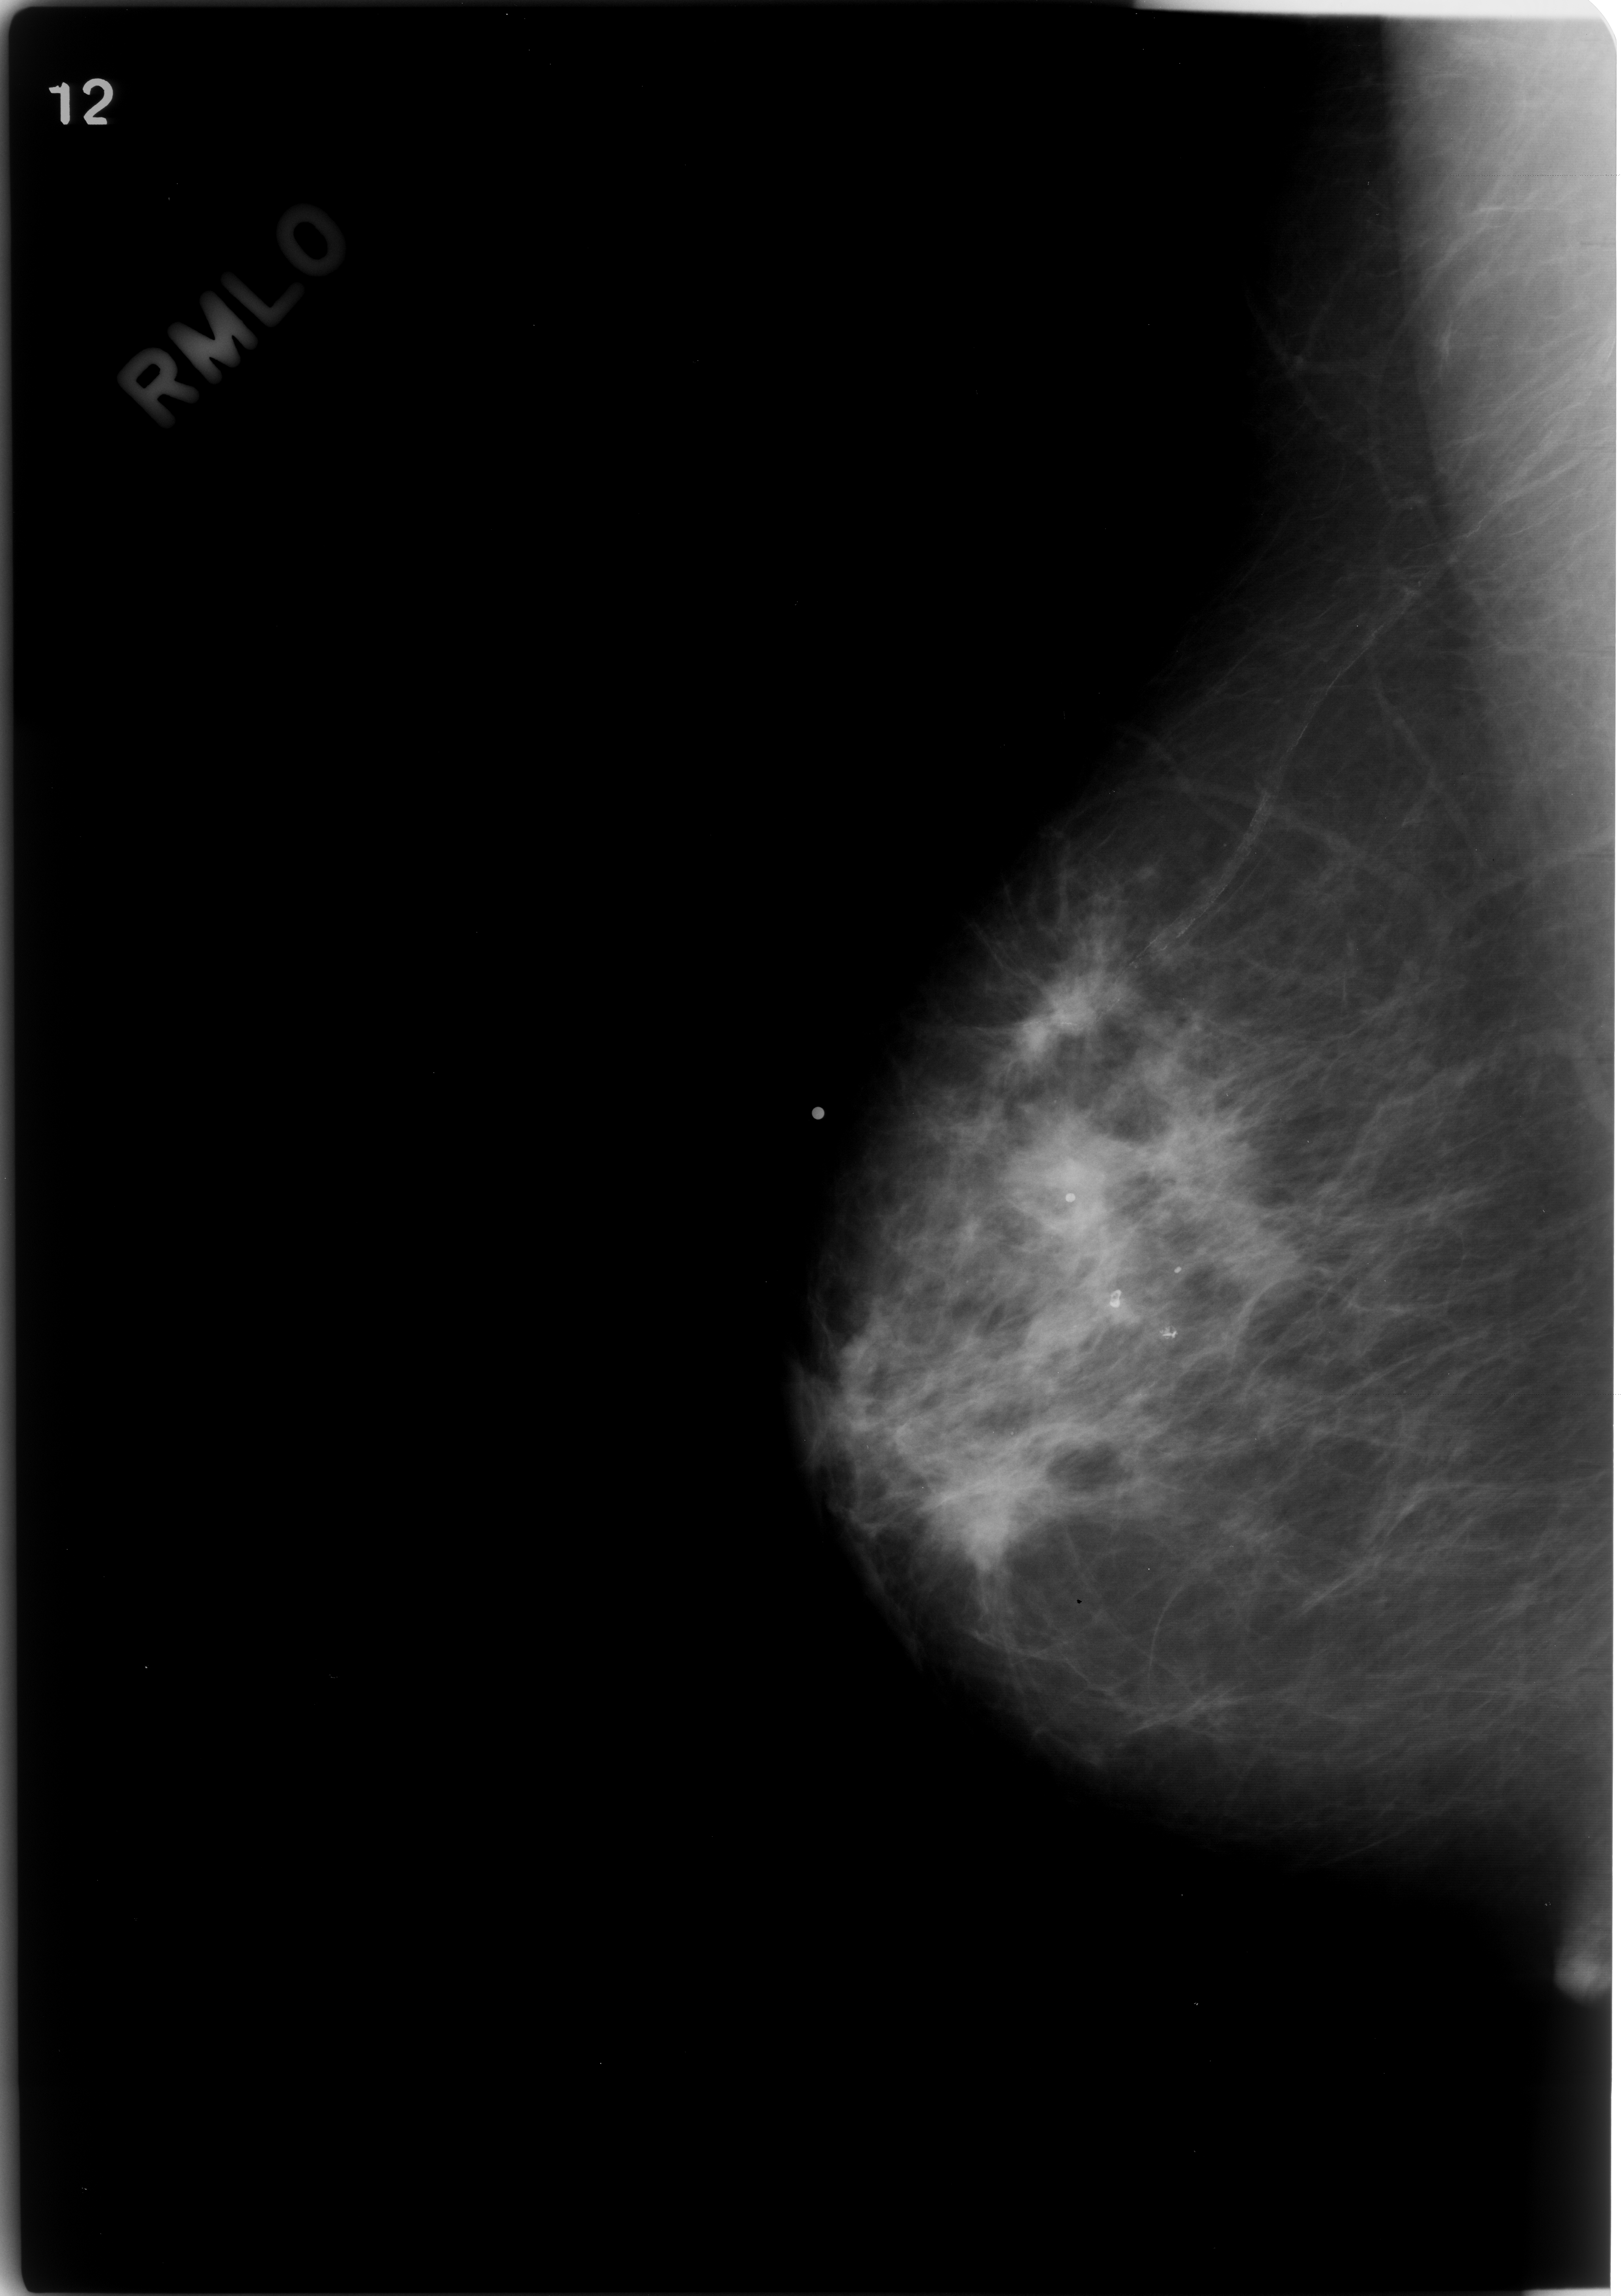
Scanned film-screen mammogram; right breast; mediolateral oblique (MLO) view; BI-RADS breast density category 2 (scale 1–4).
Abnormality record for this image: mass, shape asymmetric breast tissue, margins ill defined; BI-RADS assessment category 5; subtlety rating 5 on a 1 (subtle) to 5 (obvious) scale; pathology result (as recorded, not read from the image): malignant.